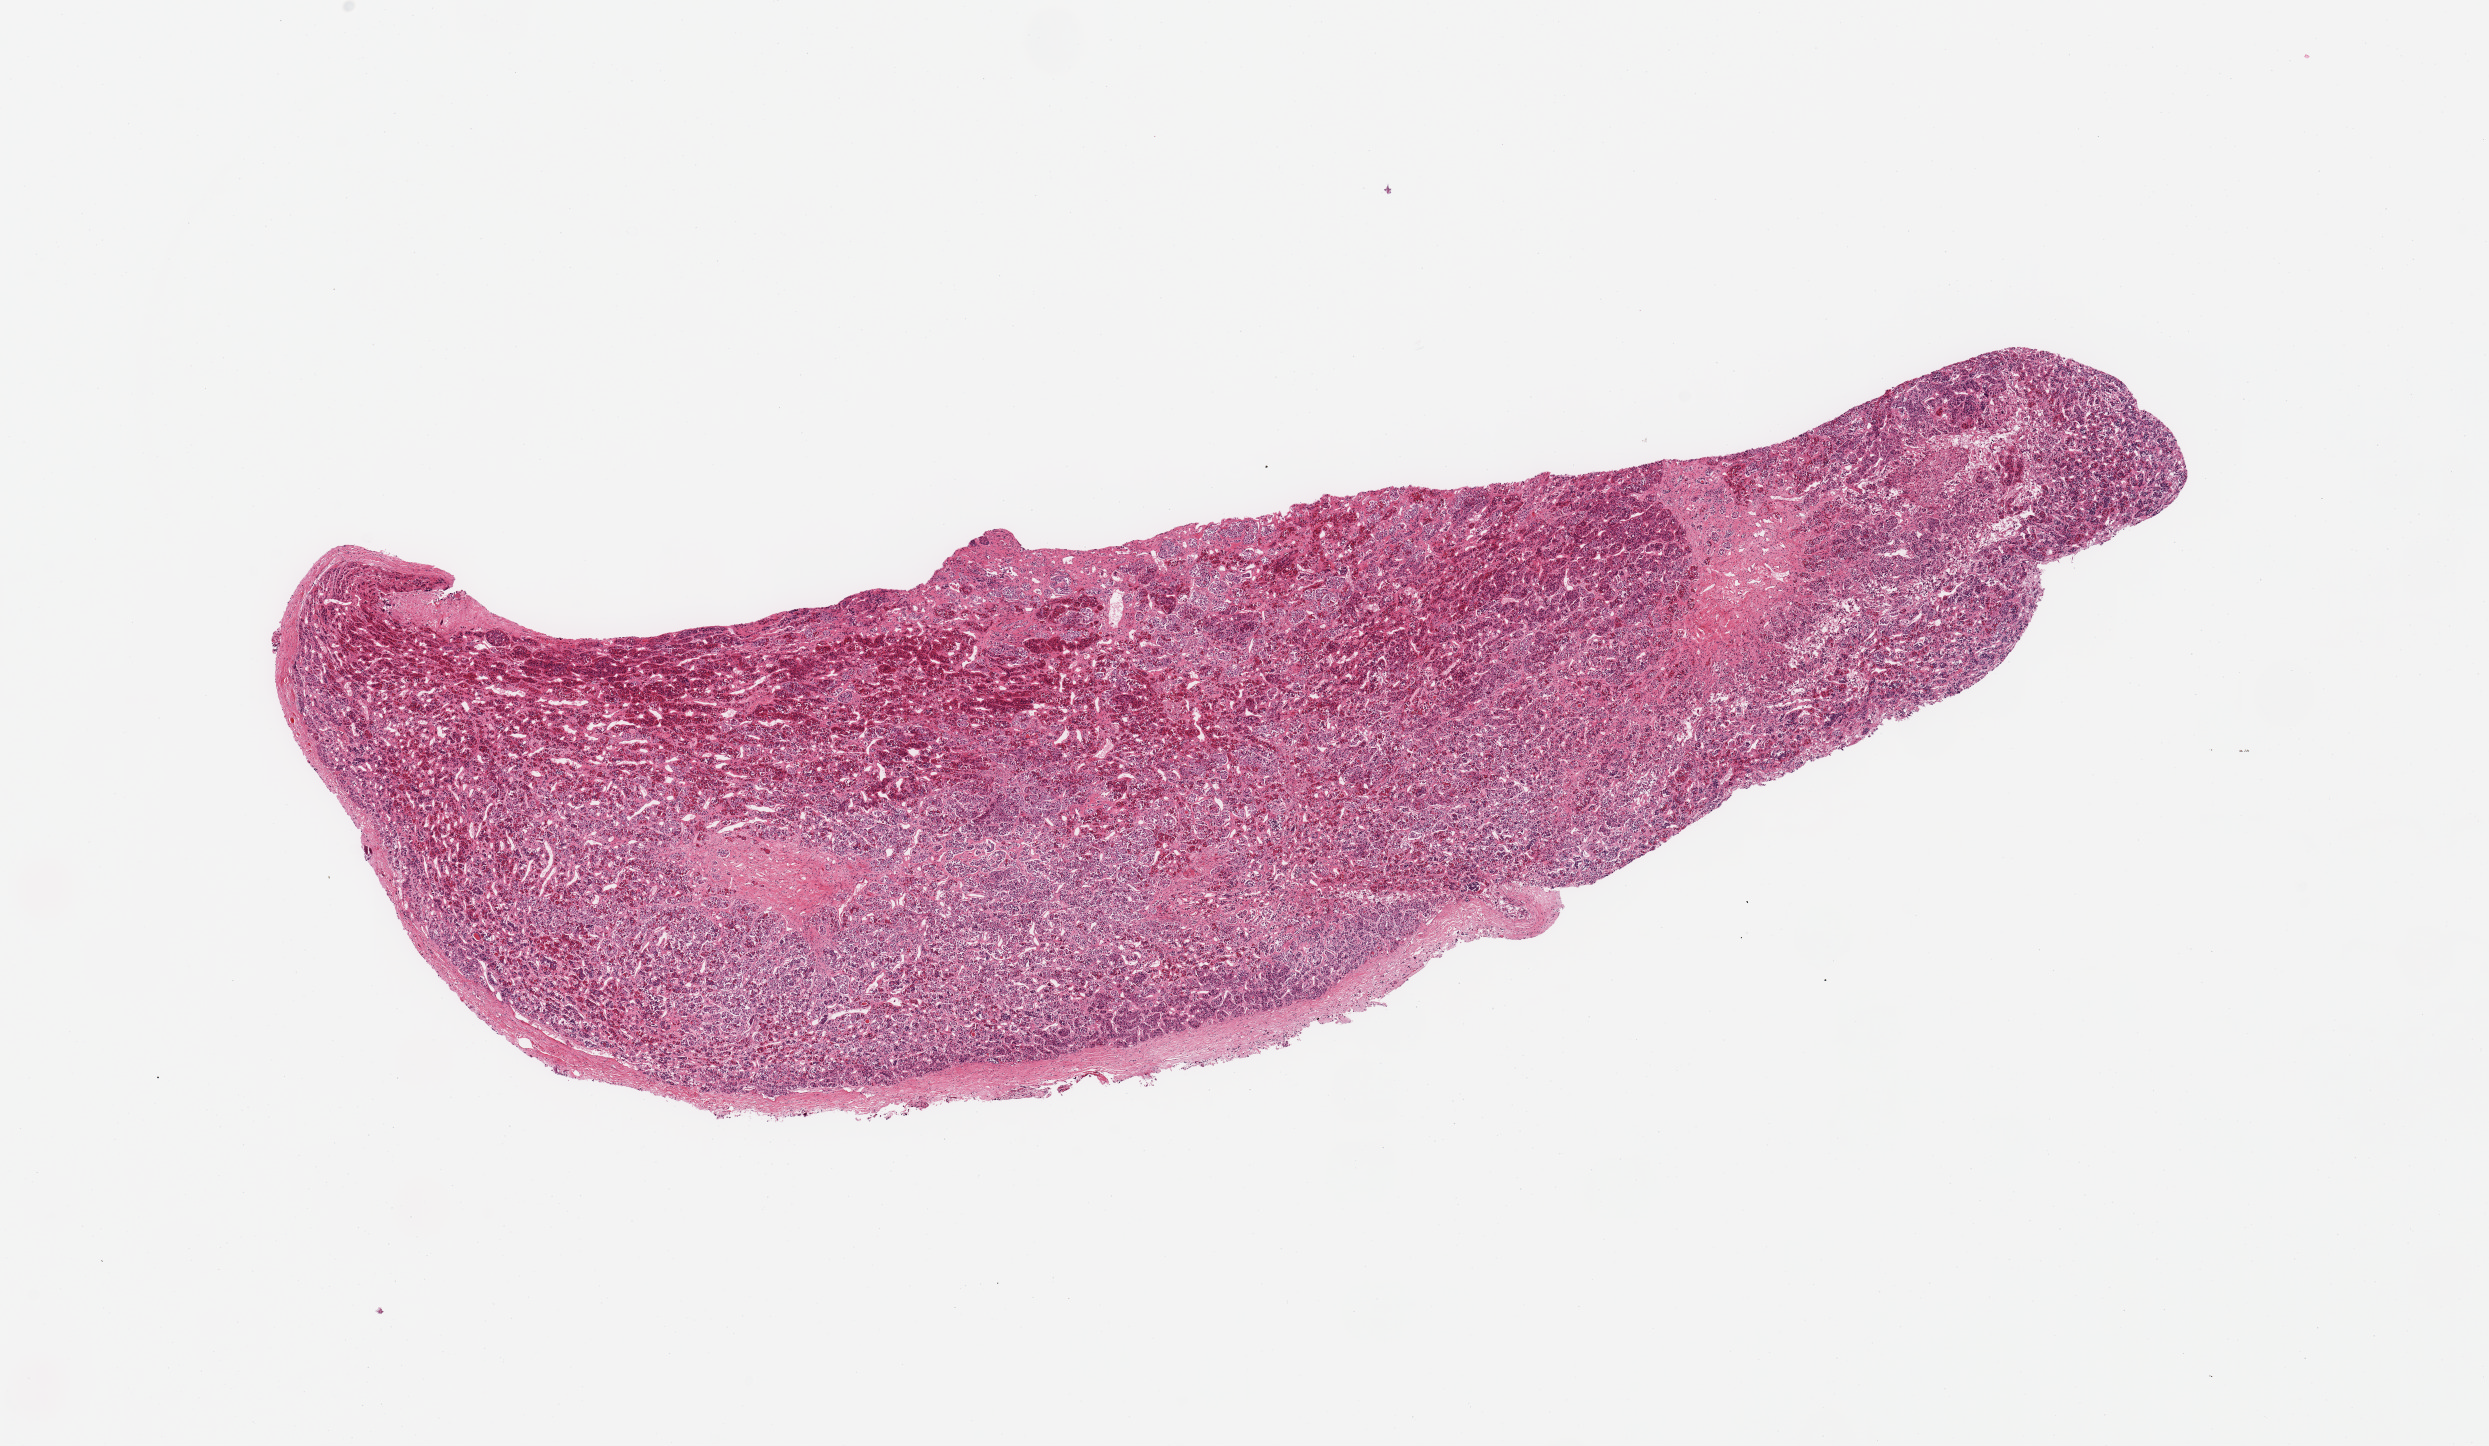
H&E whole-slide image, a low-resolution overview of the entire scanned area, about 19.7 x 11.4 mm, PAXgene-fixed paraffin-embedded (PFPE) section, sampled site (target tissue): pituitary, donor tissue sample. Donor: male.
Pathologist's review note for this sample: 1 piece, all adenohypophysis.